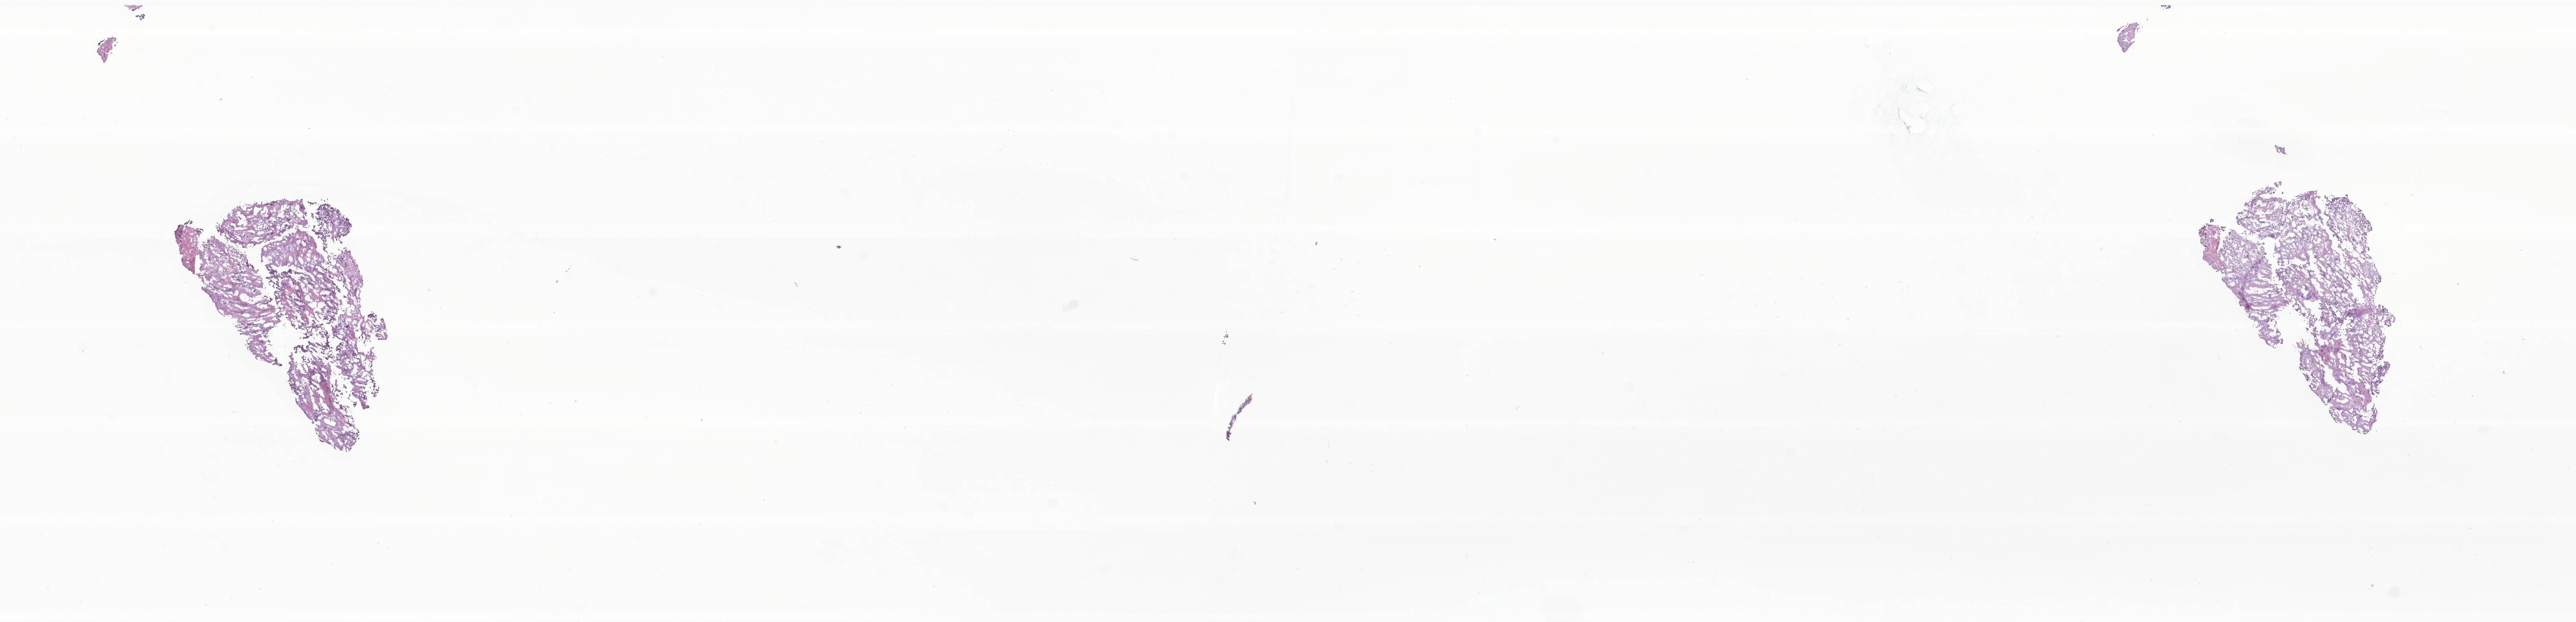
Whole-slide image, haematoxylin and eosin stain of tumor tissue from the soft tissue, low-resolution overview of the scanned area, about 28.3 x 6.8 mm; cryosection (OCT / tissue freezing medium). Patient: female, age 179 months (14 years 11 months).
Diagnosis (ICD-O-3 morphology term): Rhabdomyosarcoma, NOS.